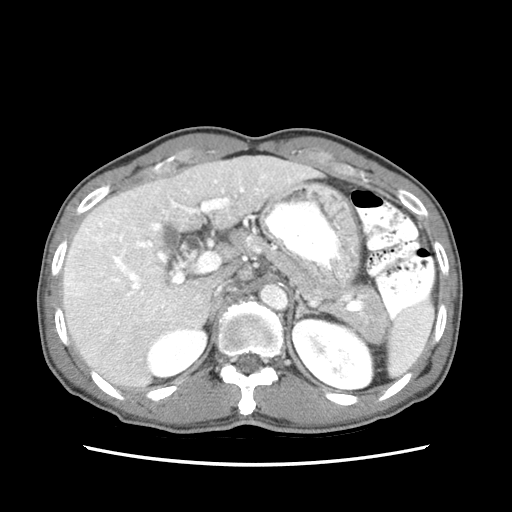
Contrast-enhanced abdominal CT (liver protocol), one axial slice; position 43 of 79 along the scan axis; reconstruction kernel STANDARD; 120 kVp; soft-tissue window (W 400 / L 40 HU); 512 × 512 image matrix. Case-level facts recorded for this patient, not image findings: diagnosis: hepatocellular carcinoma (patient treated with transarterial chemoembolisation; whether this scan precedes or follows treatment is not stated here); TNM stage (as recorded): Stage-IIIB; Child-Pugh class: A; tumour differentiation: moderately differentiated; tumour nodularity: multinodular.
Outlined on this slice (semi-automatically segmented with operator editing):
- liver parenchyma outside the tumour (the mass and vessels are separate outlines, so this box may not span the whole liver): bounding box <62,154,323,390> (left, top, right, bottom; pixels)
- mass: <63,220,123,292>
- liver vessels: <72,166,313,367>